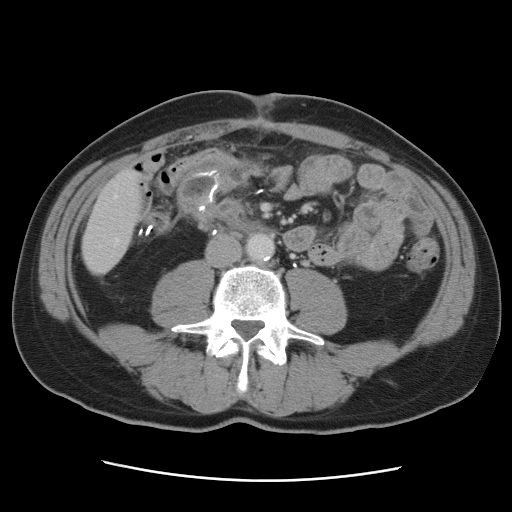
Contrast-enhanced abdominal CT, one axial slice; position 12 of 89 along the scan axis; intravenous contrast given; soft-tissue window (W 400 / L 40 HU); 5 mm slice thickness; 512 × 512 image matrix, field of view 366 × 366 mm. Male patient, age 59 years. Case-level facts recorded for this patient, not image findings: diagnosis: colorectal cancer liver metastases, imaged before liver resection; multiple liver metastases: yes; largest metastasis: 0.6 cm; chemotherapy before resection: no.
Outlined on this slice (manually delineated by an expert):
- hepatic veins: bounding box [x1, y1, x2, y2] px = [114, 196, 120, 245]
- liver: [83, 170, 143, 273]
- planned liver remnant (the part of the liver to remain after resection): [83, 170, 143, 258]